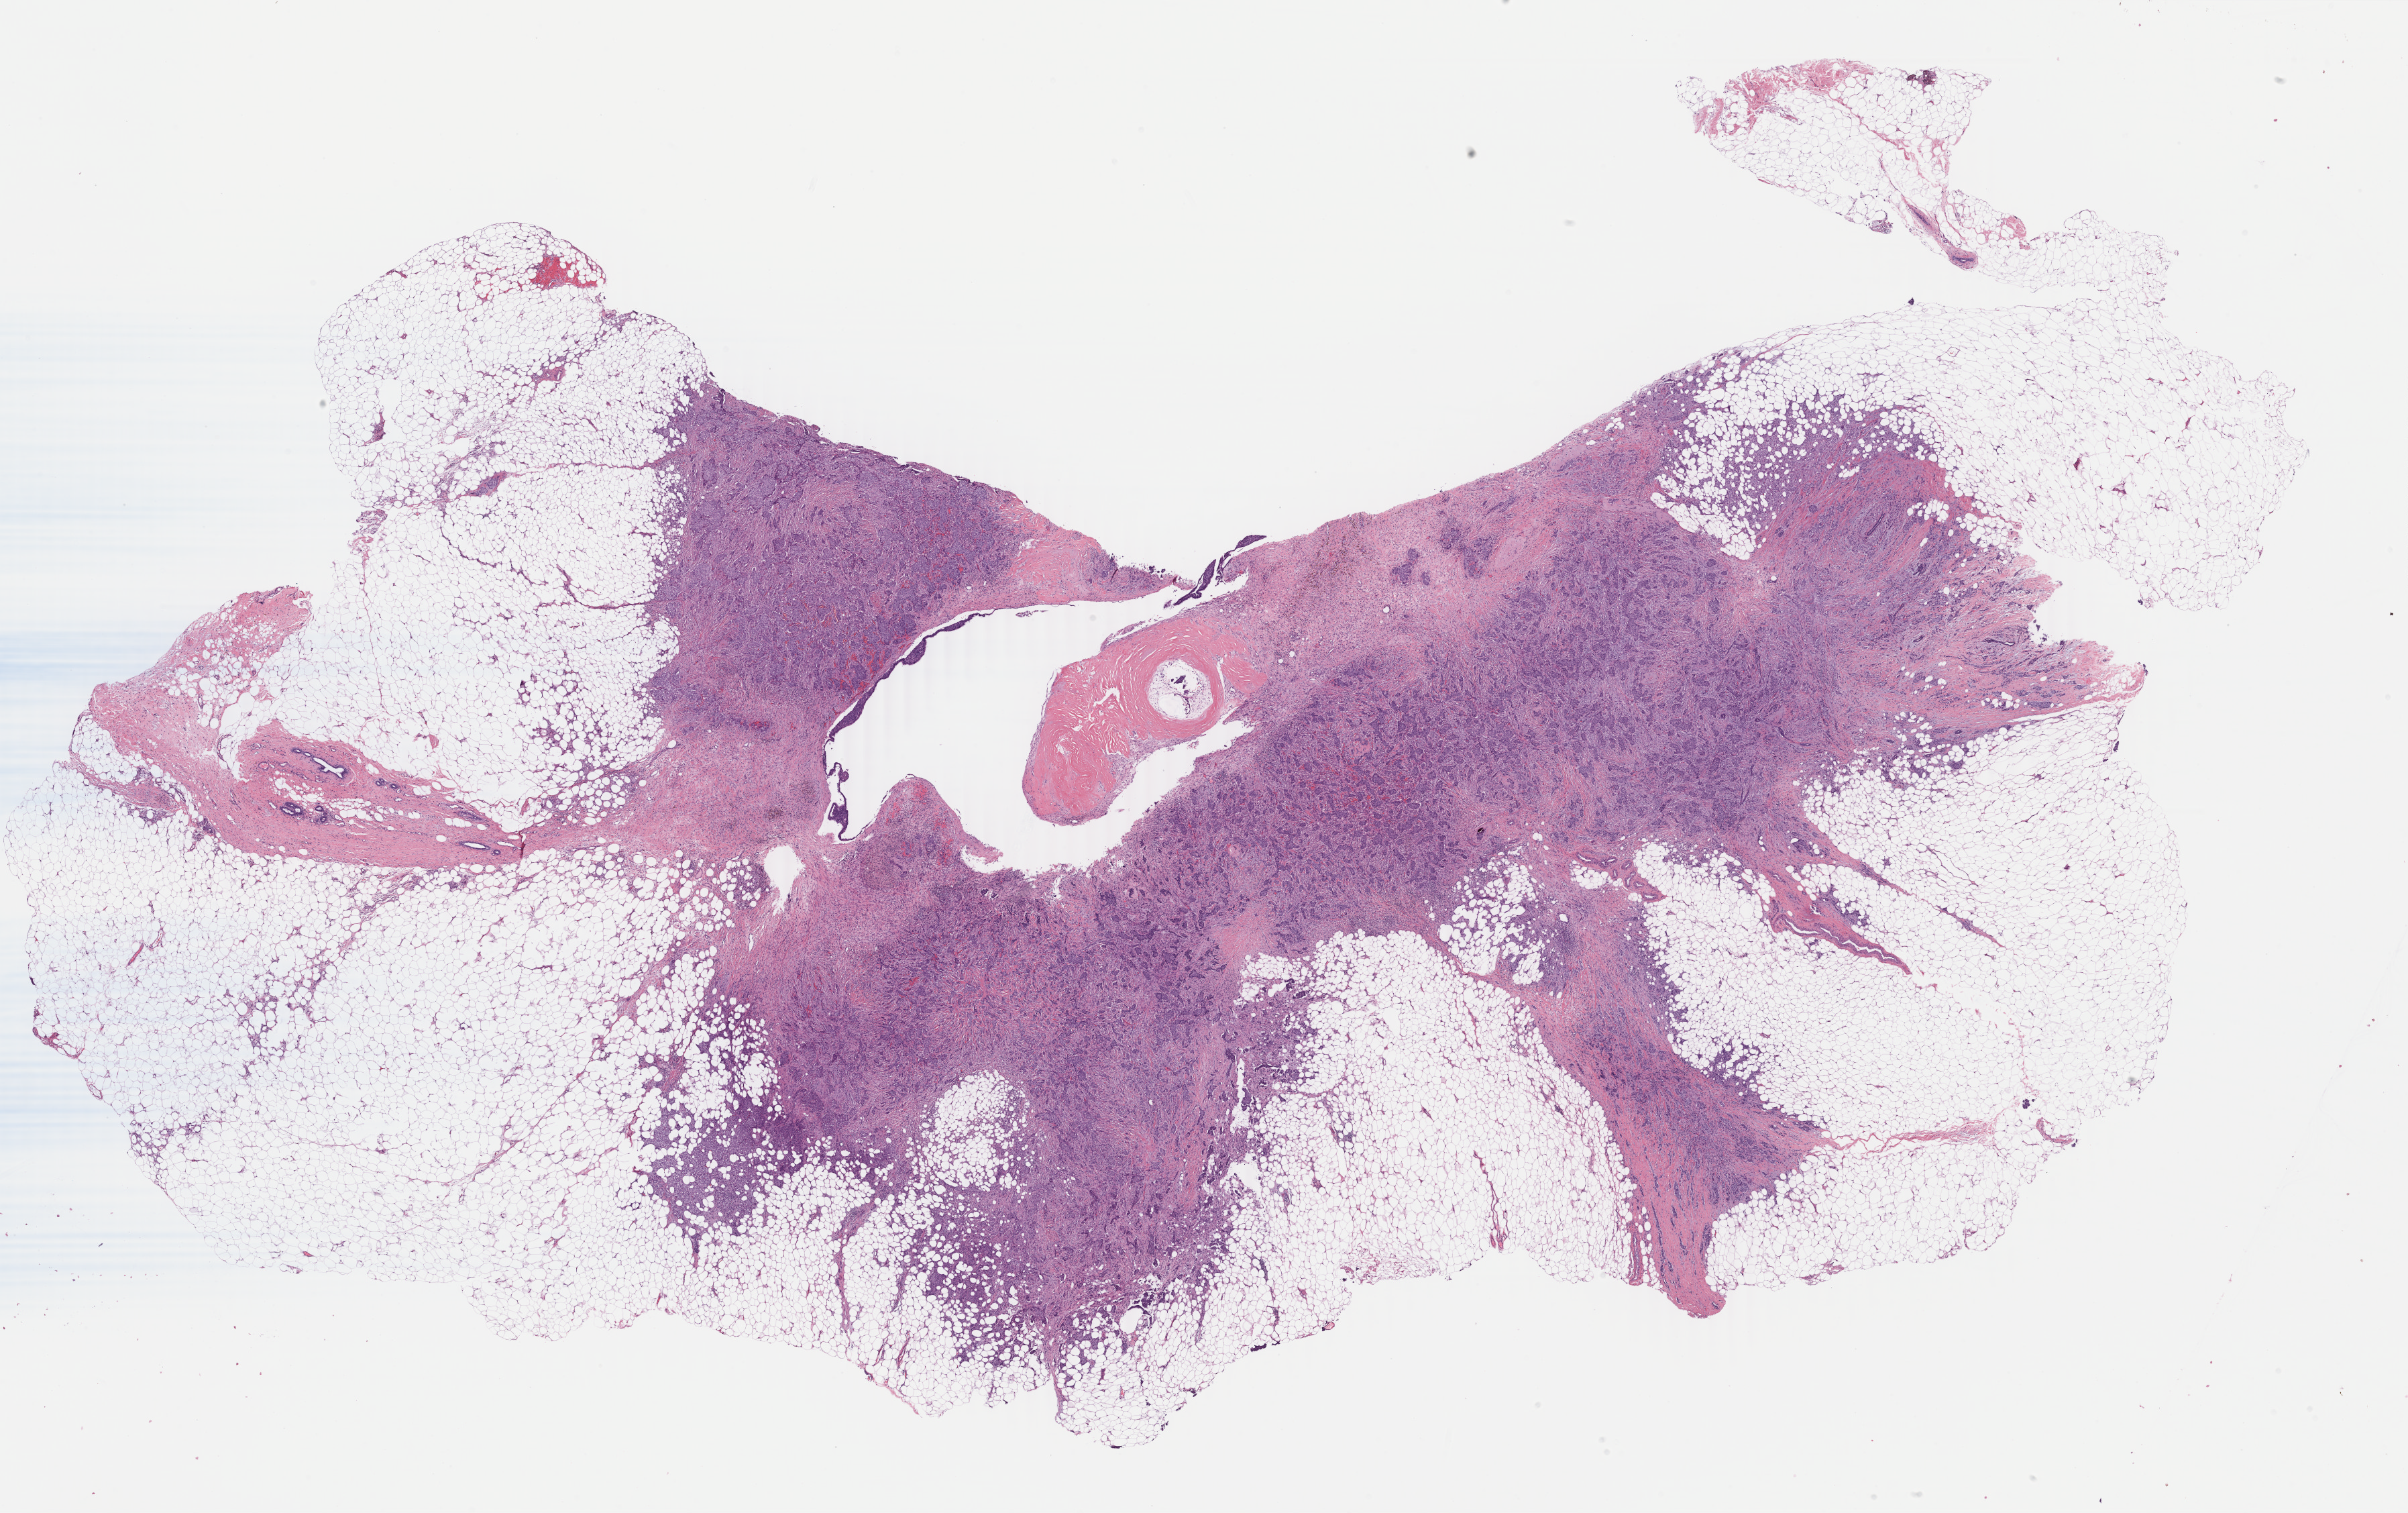
Whole-slide histology image, H&E-stained, whole scanned area (about 28.6 x 17.9 mm) shown as a low-resolution overview. Formalin-fixed paraffin-embedded (FFPE) diagnostic section. Breast, primary tumour sample. Patient: female, age at initial diagnosis 63 years.
AJCC pathologic stage: IIA. Histologic diagnosis: Infiltrating duct carcinoma, NOS. Lymph nodes positive (case pathology): 0 of 3 examined. Laterality: right.